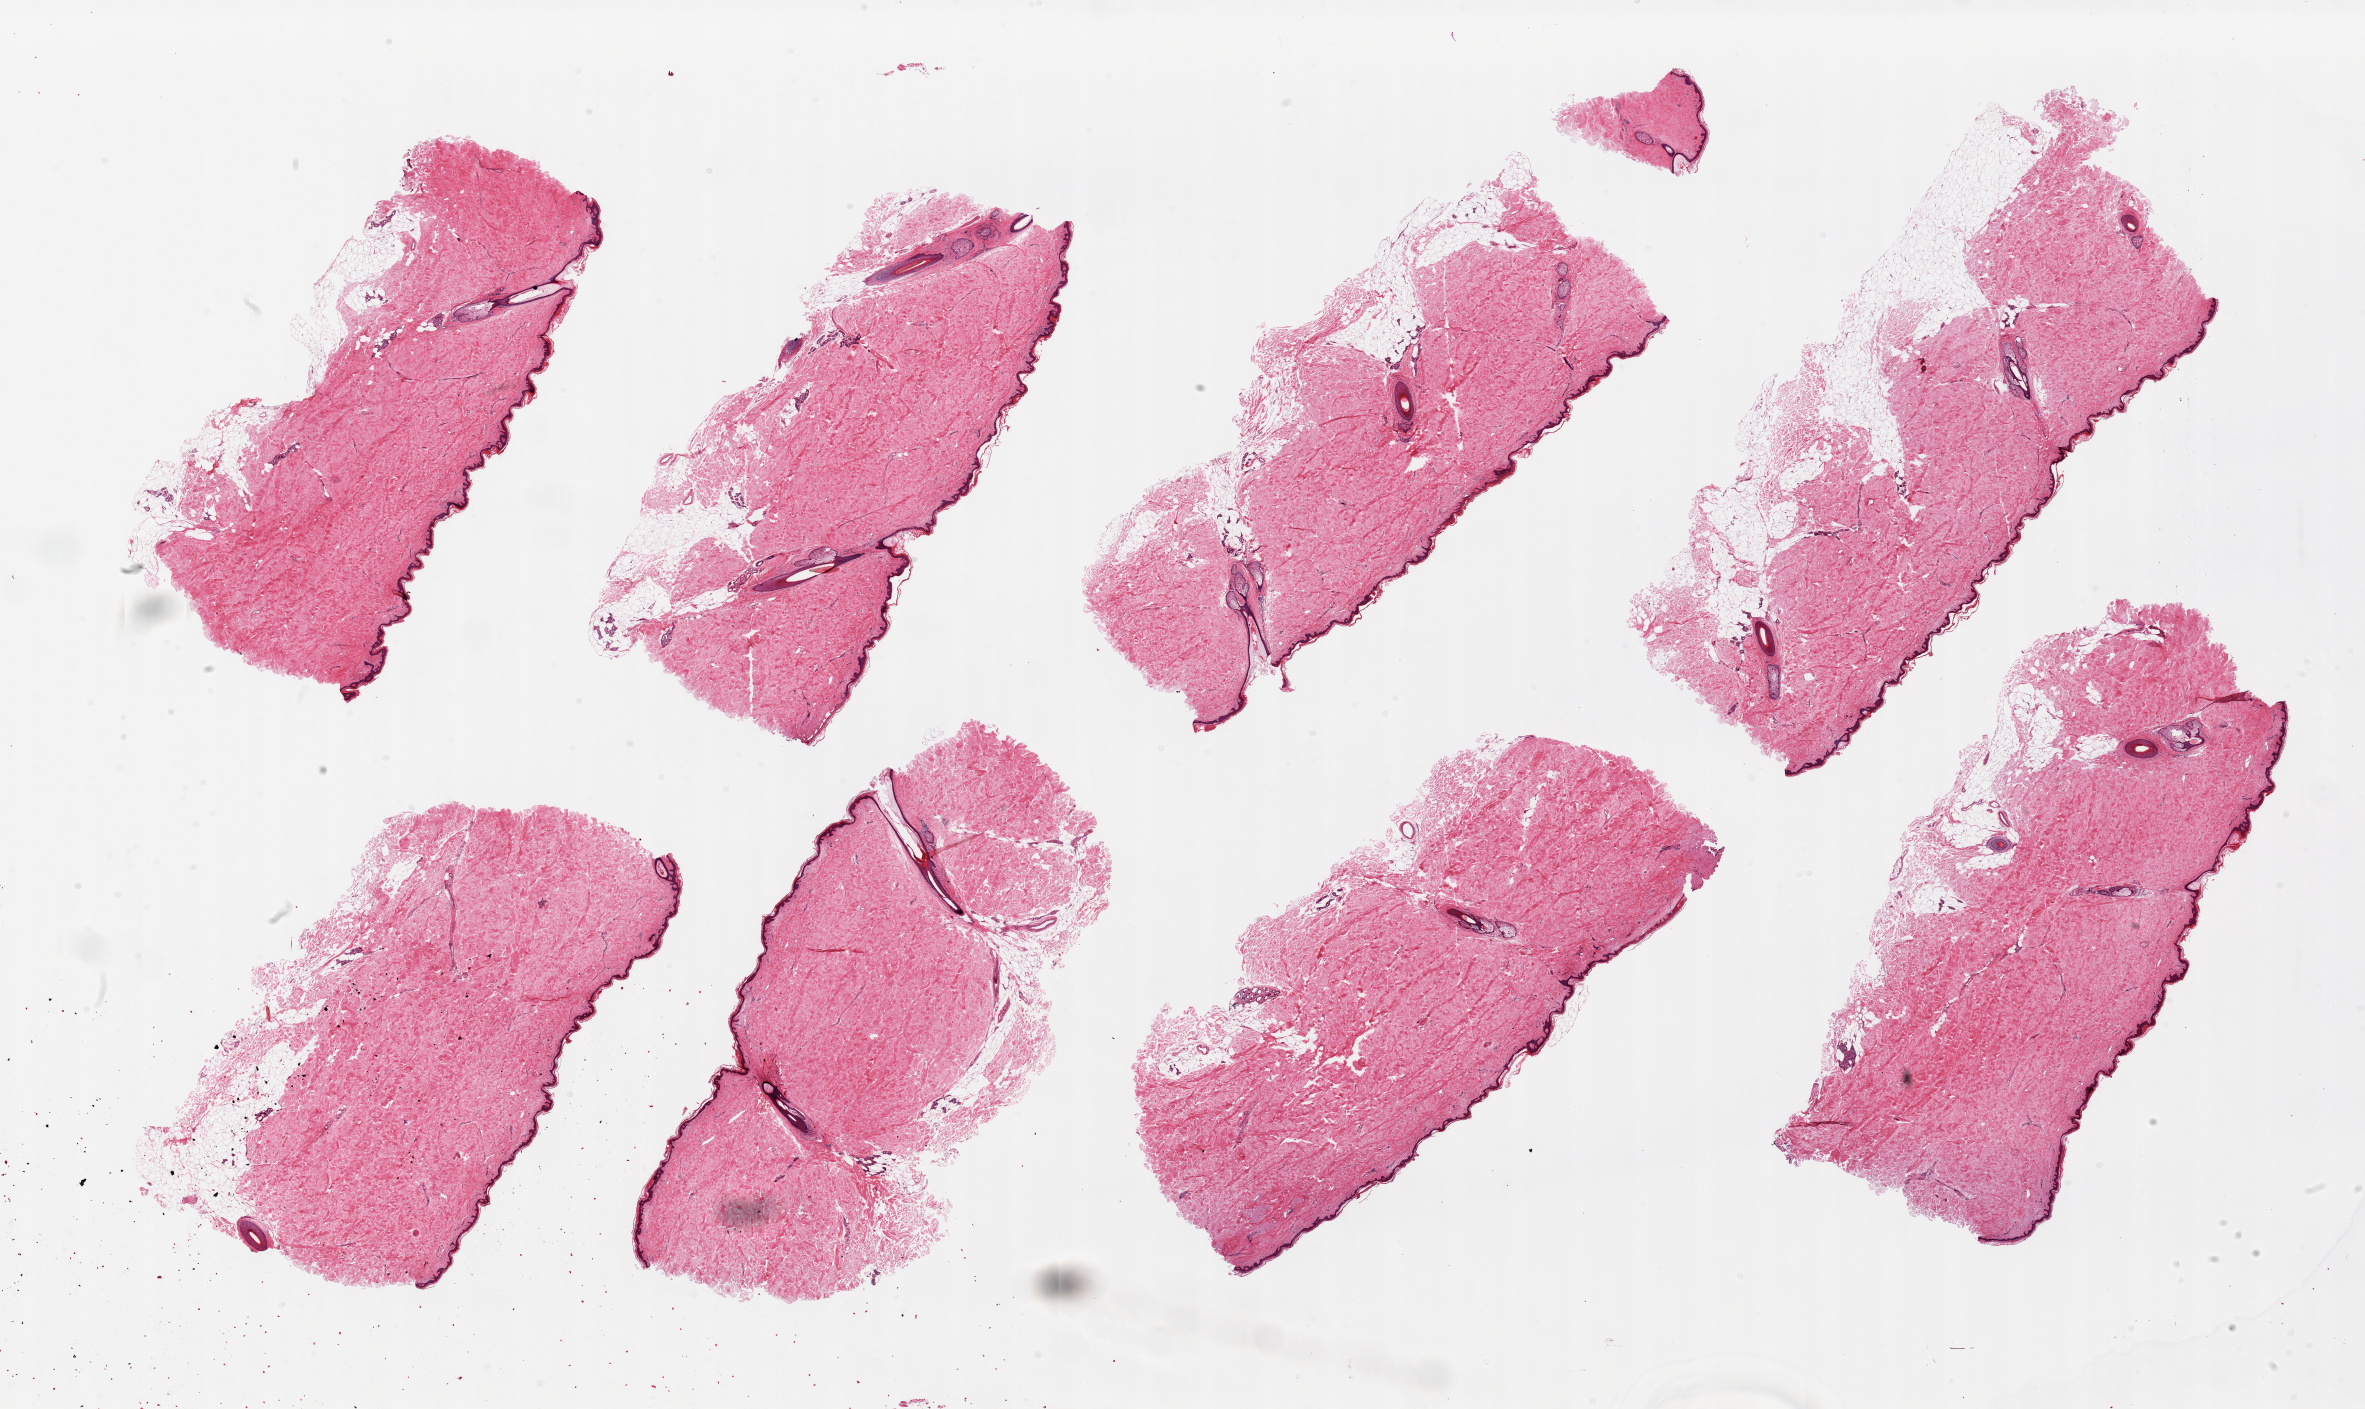
Whole-slide image, haematoxylin and eosin stain, a low-resolution overview of the entire scanned area, about 37.4 x 22.3 mm. PAXgene-fixed paraffin-embedded (PFPE) section. Target tissue: skin of suprapubic region. Tissue donor sample. Male donor.
Pathologist's review note for this sample: 8 pieces, 10x4mm. Squamous epithelium is <1% thickness.